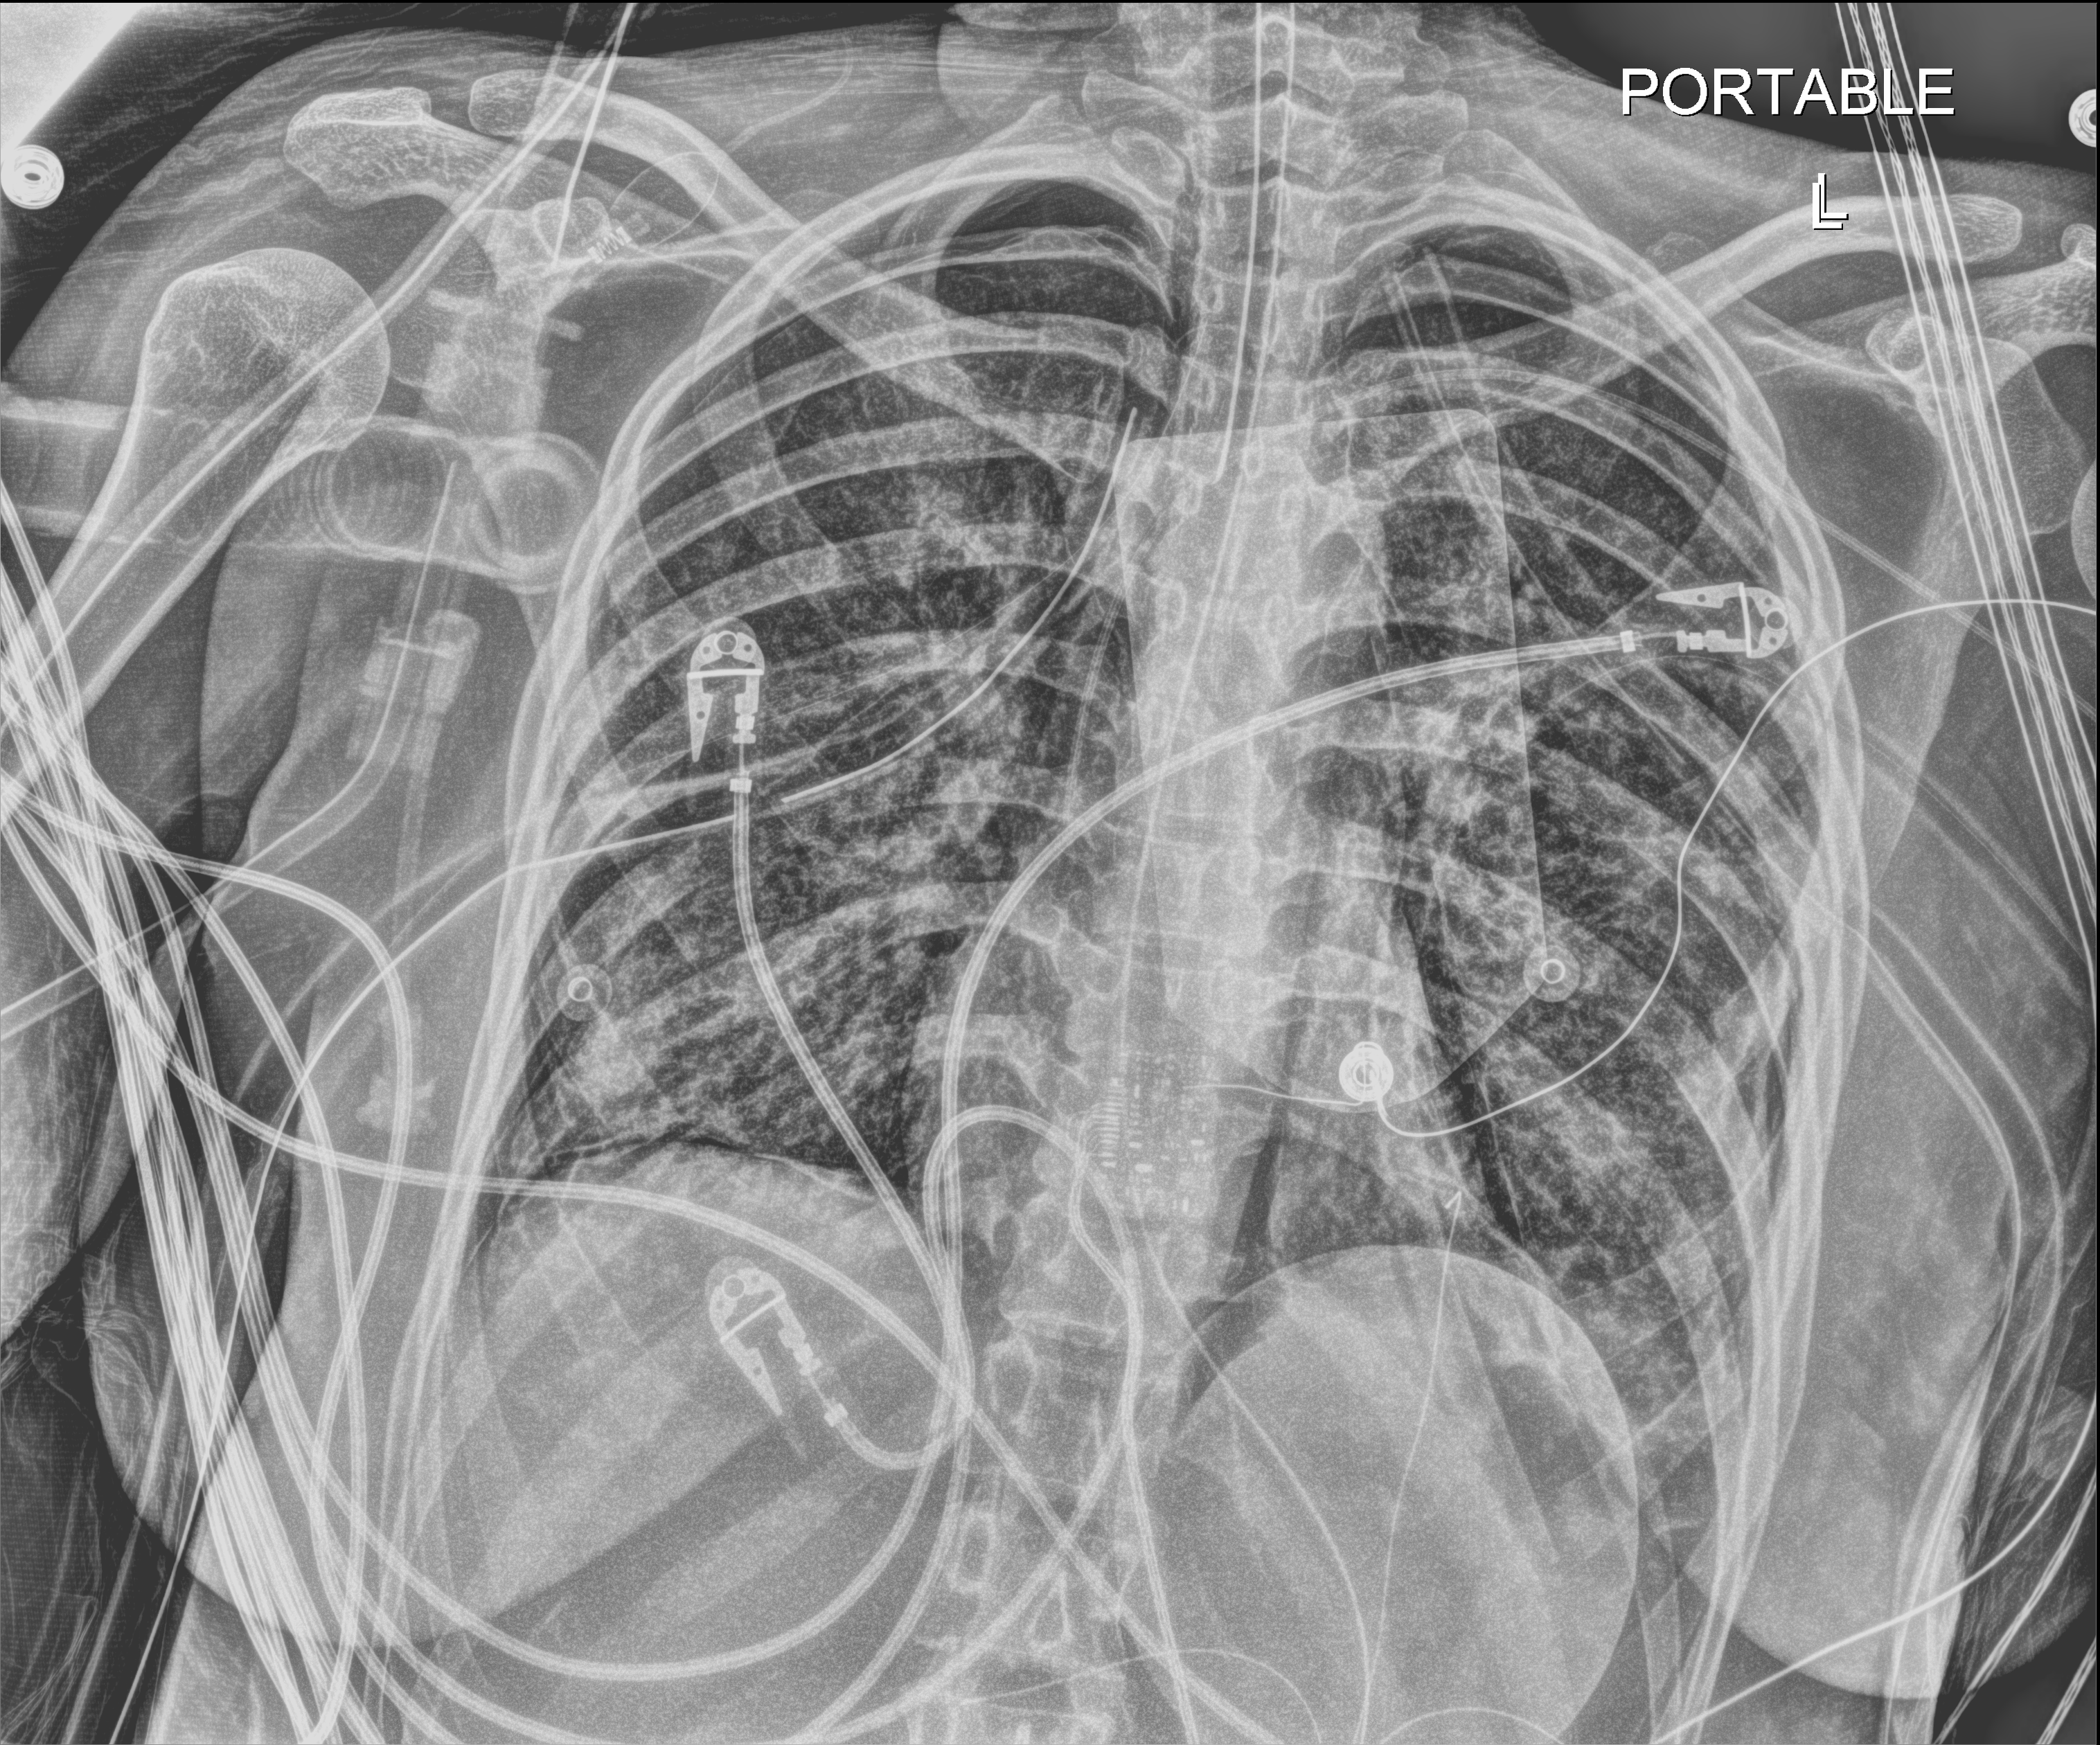
Chest X-ray (portable); anteroposterior (AP) projection. Patient hospitalised with COVID-19, aged 18–59 years.
Admission-level facts for this patient (not findings on this image; timing relative to this image not recorded):
- admitted to intensive care during this hospital stay: yes
- length of hospital stay: 30 days